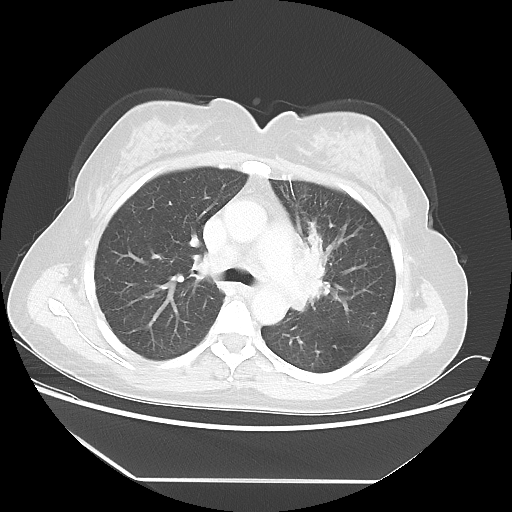
Chest CT, one axial slice. Position 34 of 52 along the scan axis. 100 kVp. Lung window (W 1500 / L -600 HU). 512 × 512 image matrix, field of view 390 × 390 mm. Patient: female, 50 years. Case-level facts recorded for this patient, not image findings: clinical TNM (as recorded): T2 N3 M0.
Annotated regions visible in this slice (rectangle marked by the reading radiologist):
- lung tumour (recorded histology: adenocarcinoma): bounding box (x1, y1, x2, y2) in pixels: (282, 240, 346, 336)